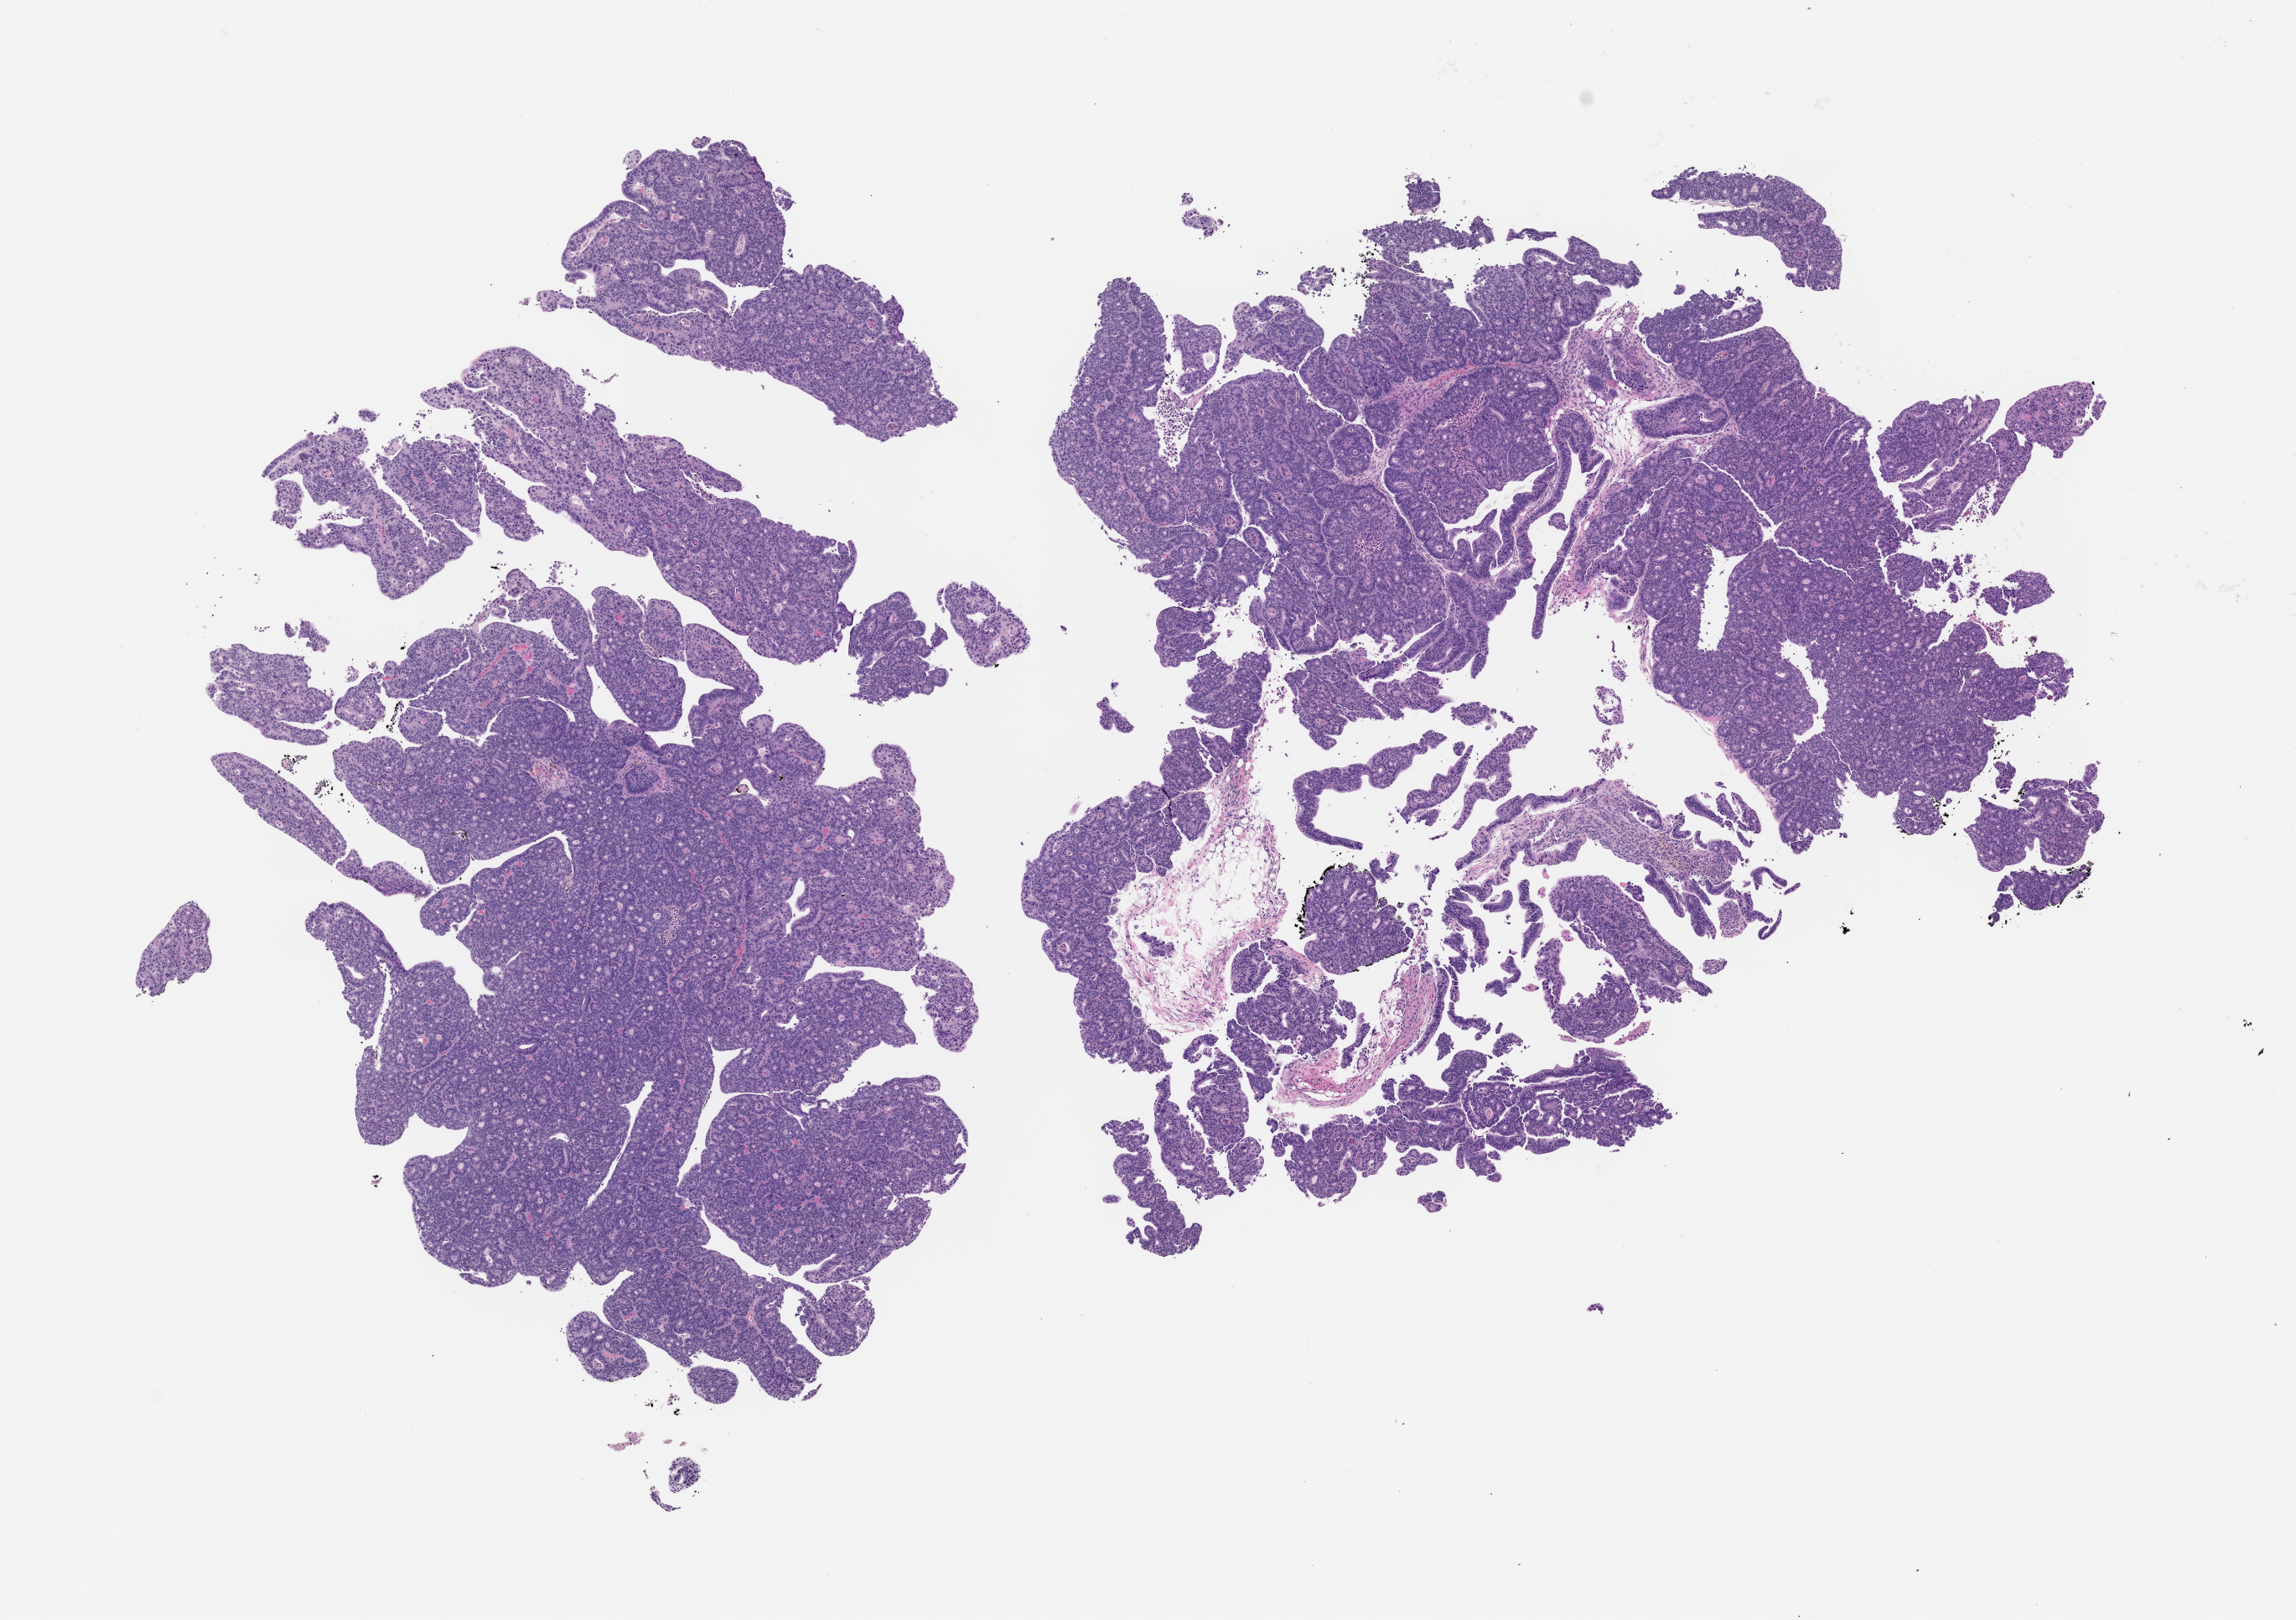
Hematoxylin and eosin (H&E) whole-slide image of a patient-derived xenograft (PDX) tumor grown in a mouse, passage 1, shown as a low-resolution overview of the whole scanned area (about 11.0 x 7.8 mm), formalin-fixed paraffin-embedded section, originating tumor site category: colon.
* originating patient diagnosis: Colon Adenocarcinoma